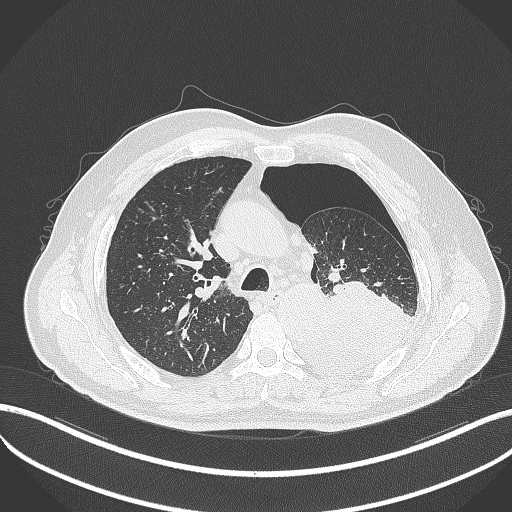
Chest CT, one axial slice; position 355 of 464 along the scan axis; reconstruction kernel B70f; lung window (W 1500 / L -600 HU); 512 × 512 image matrix, field of view 400 × 400 mm. Patient: male, 76 years. From the clinical record (not read from this slice): clinical TNM (as recorded): T3 N0 M1b.
Structures marked on this image (bounding box drawn by a radiologist):
- lung tumour (recorded histology: adenocarcinoma): bounding box [x1, y1, x2, y2] px = [308, 278, 416, 380]